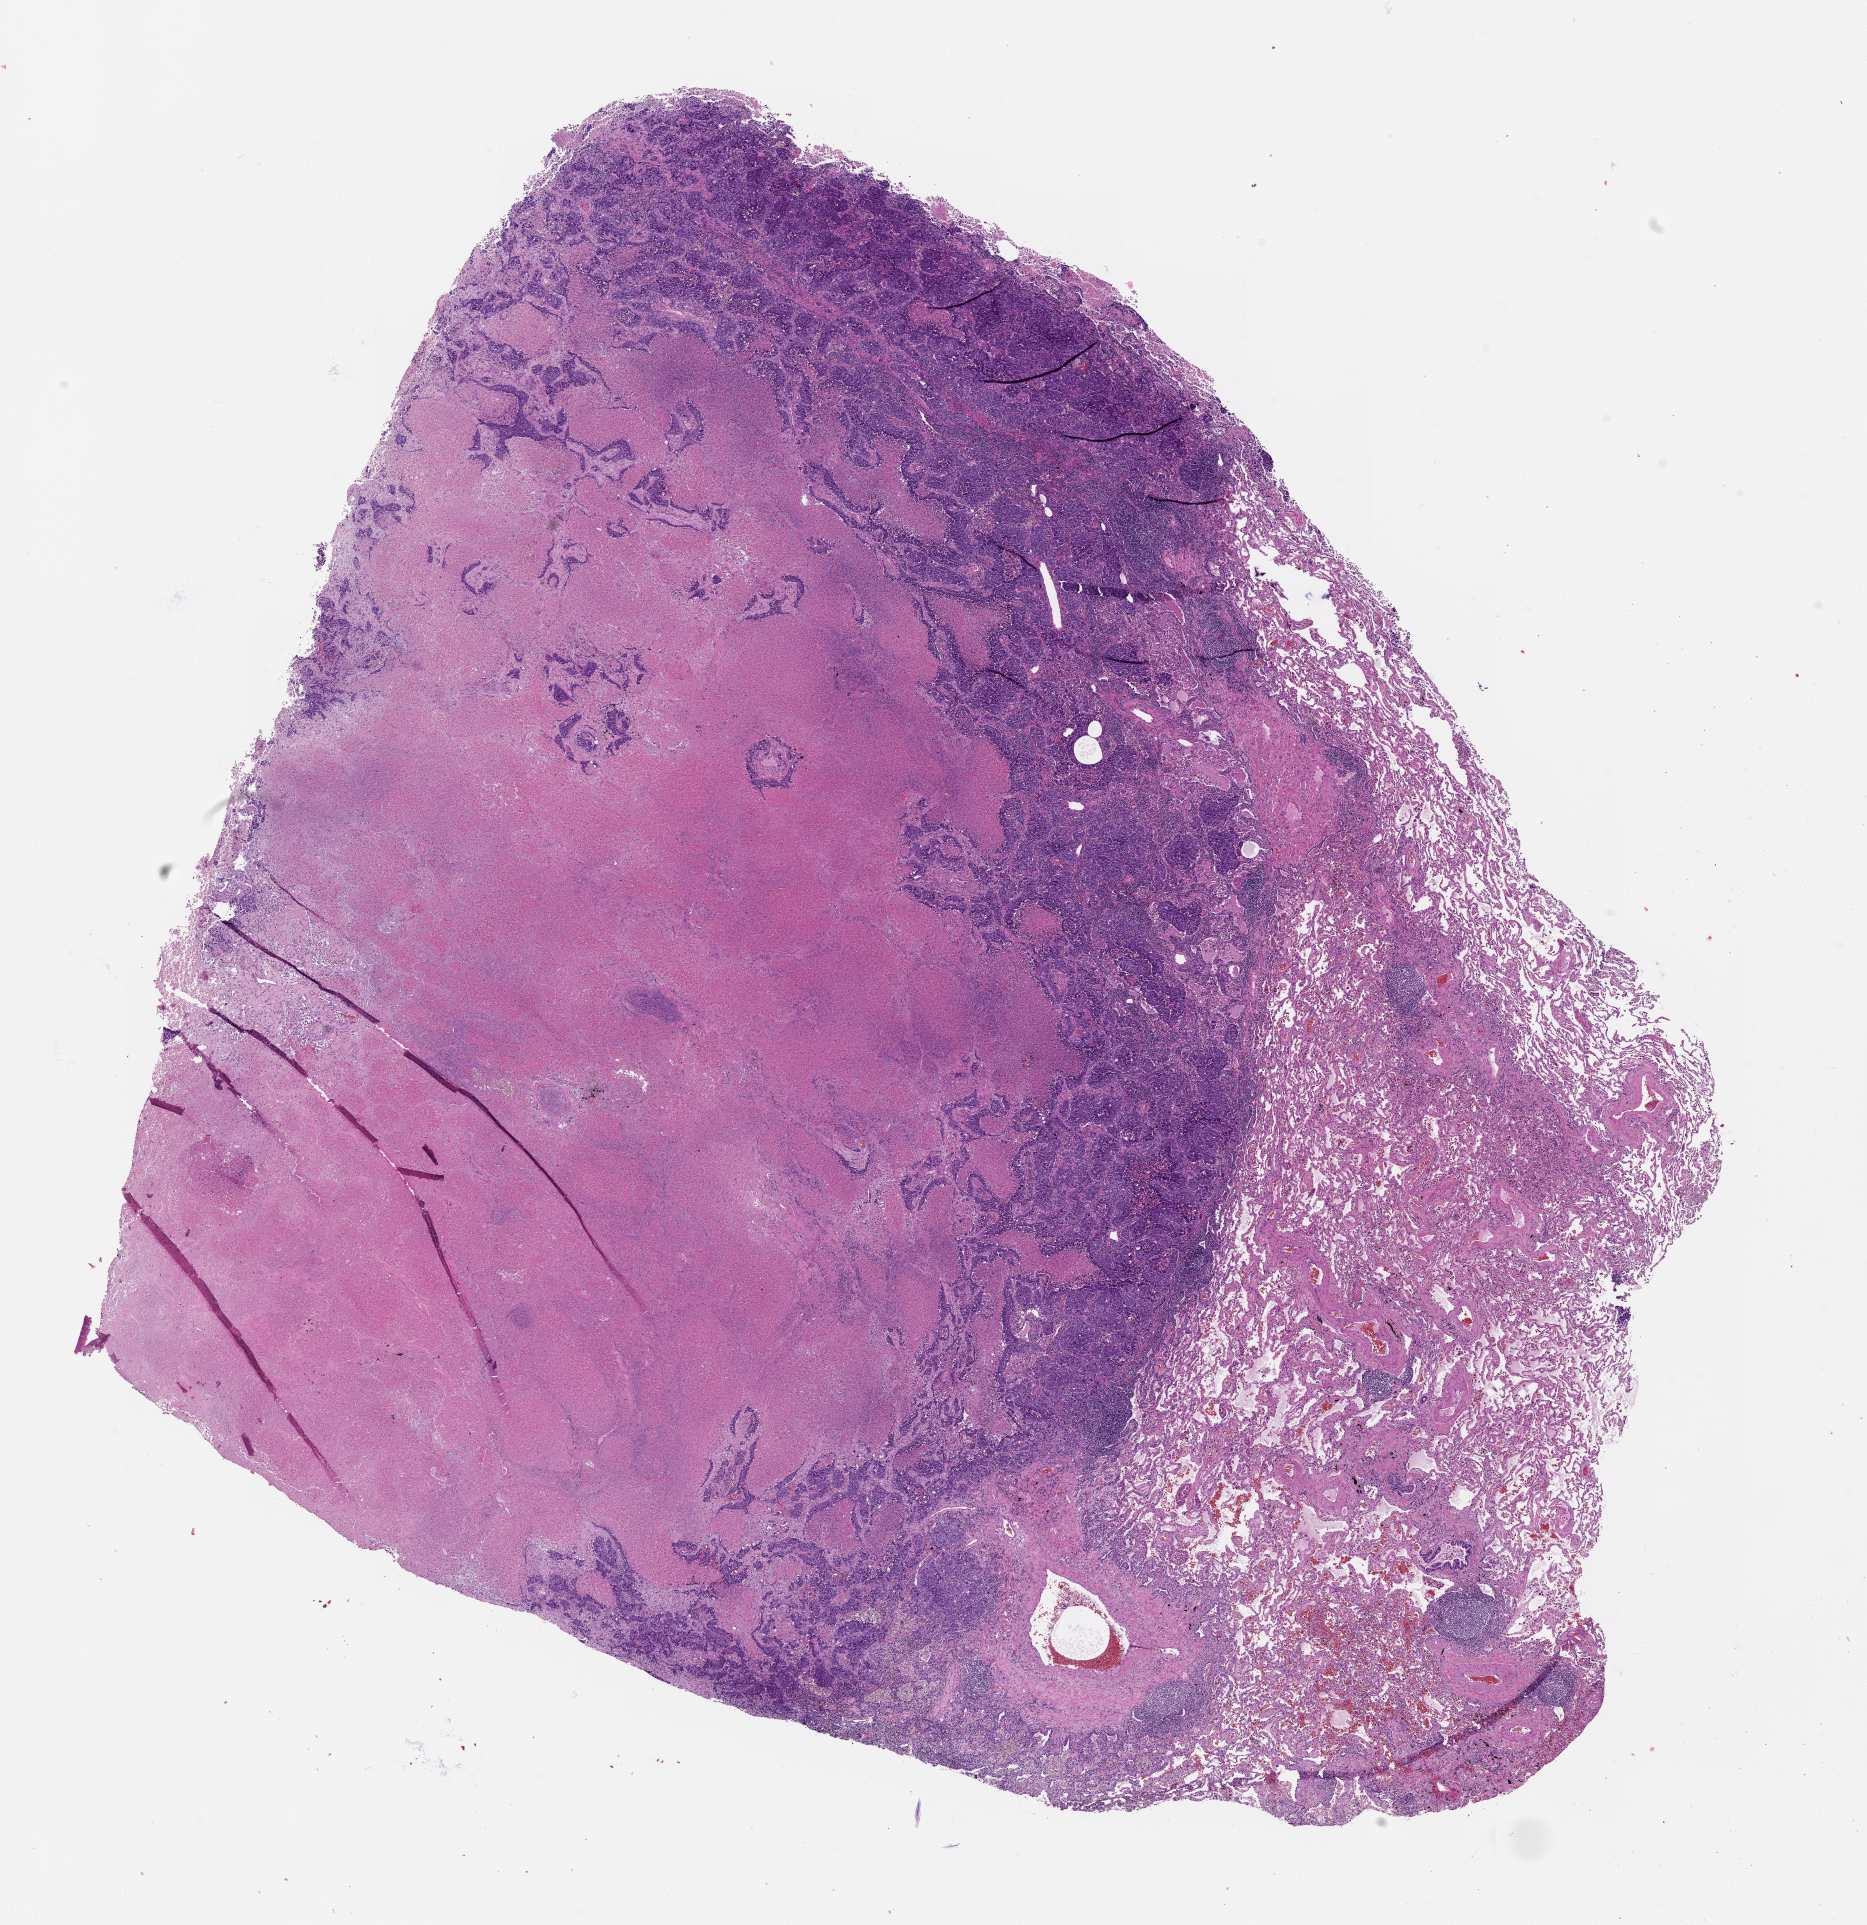
Whole-slide histology image, Hematoxylin and eosin (H&E) stained, a low-resolution overview of the entire scanned area, about 15.0 x 15.5 mm; lung, tumour tissue. Male, 60 y/o.
* patient diagnosis (cohort enrolment): squamous cell carcinoma (lung)